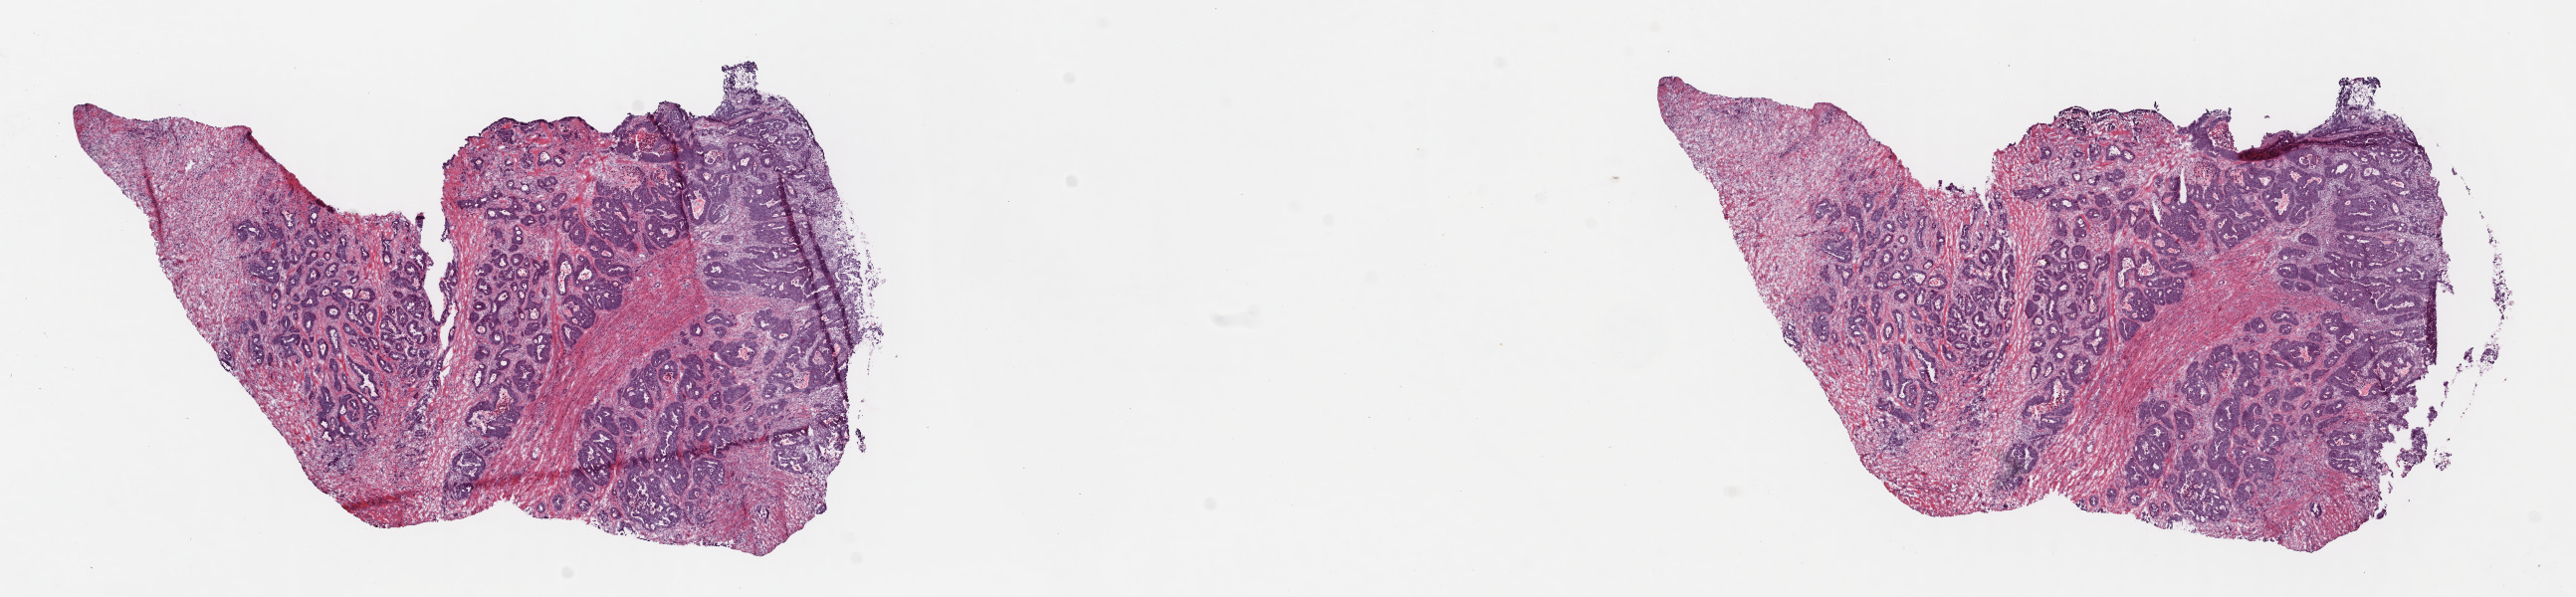
Hematoxylin and eosin (H&E) stained whole-slide image, low-resolution overview of the scanned area, about 20.3 x 4.7 mm (from a 40x scan), frozen section, colon, primary tumour sample. Male patient; age at initial diagnosis 59 years. Composition of this section per pathologist review: tumour cells 70%, tumour nuclei 70%, normal cells 0%, stromal cells 27%, necrosis 3%. Inflammatory infiltration, as recorded: lymphocyte infiltration 2%, monocyte infiltration 2%, neutrophil infiltration 5%.
TNM: T3 N1 M0. Diagnosis: Adenocarcinoma, NOS (transverse colon). AJCC pathologic stage: IIIB (7th edition). Lymph nodes positive (case pathology): 1 of 60 examined.